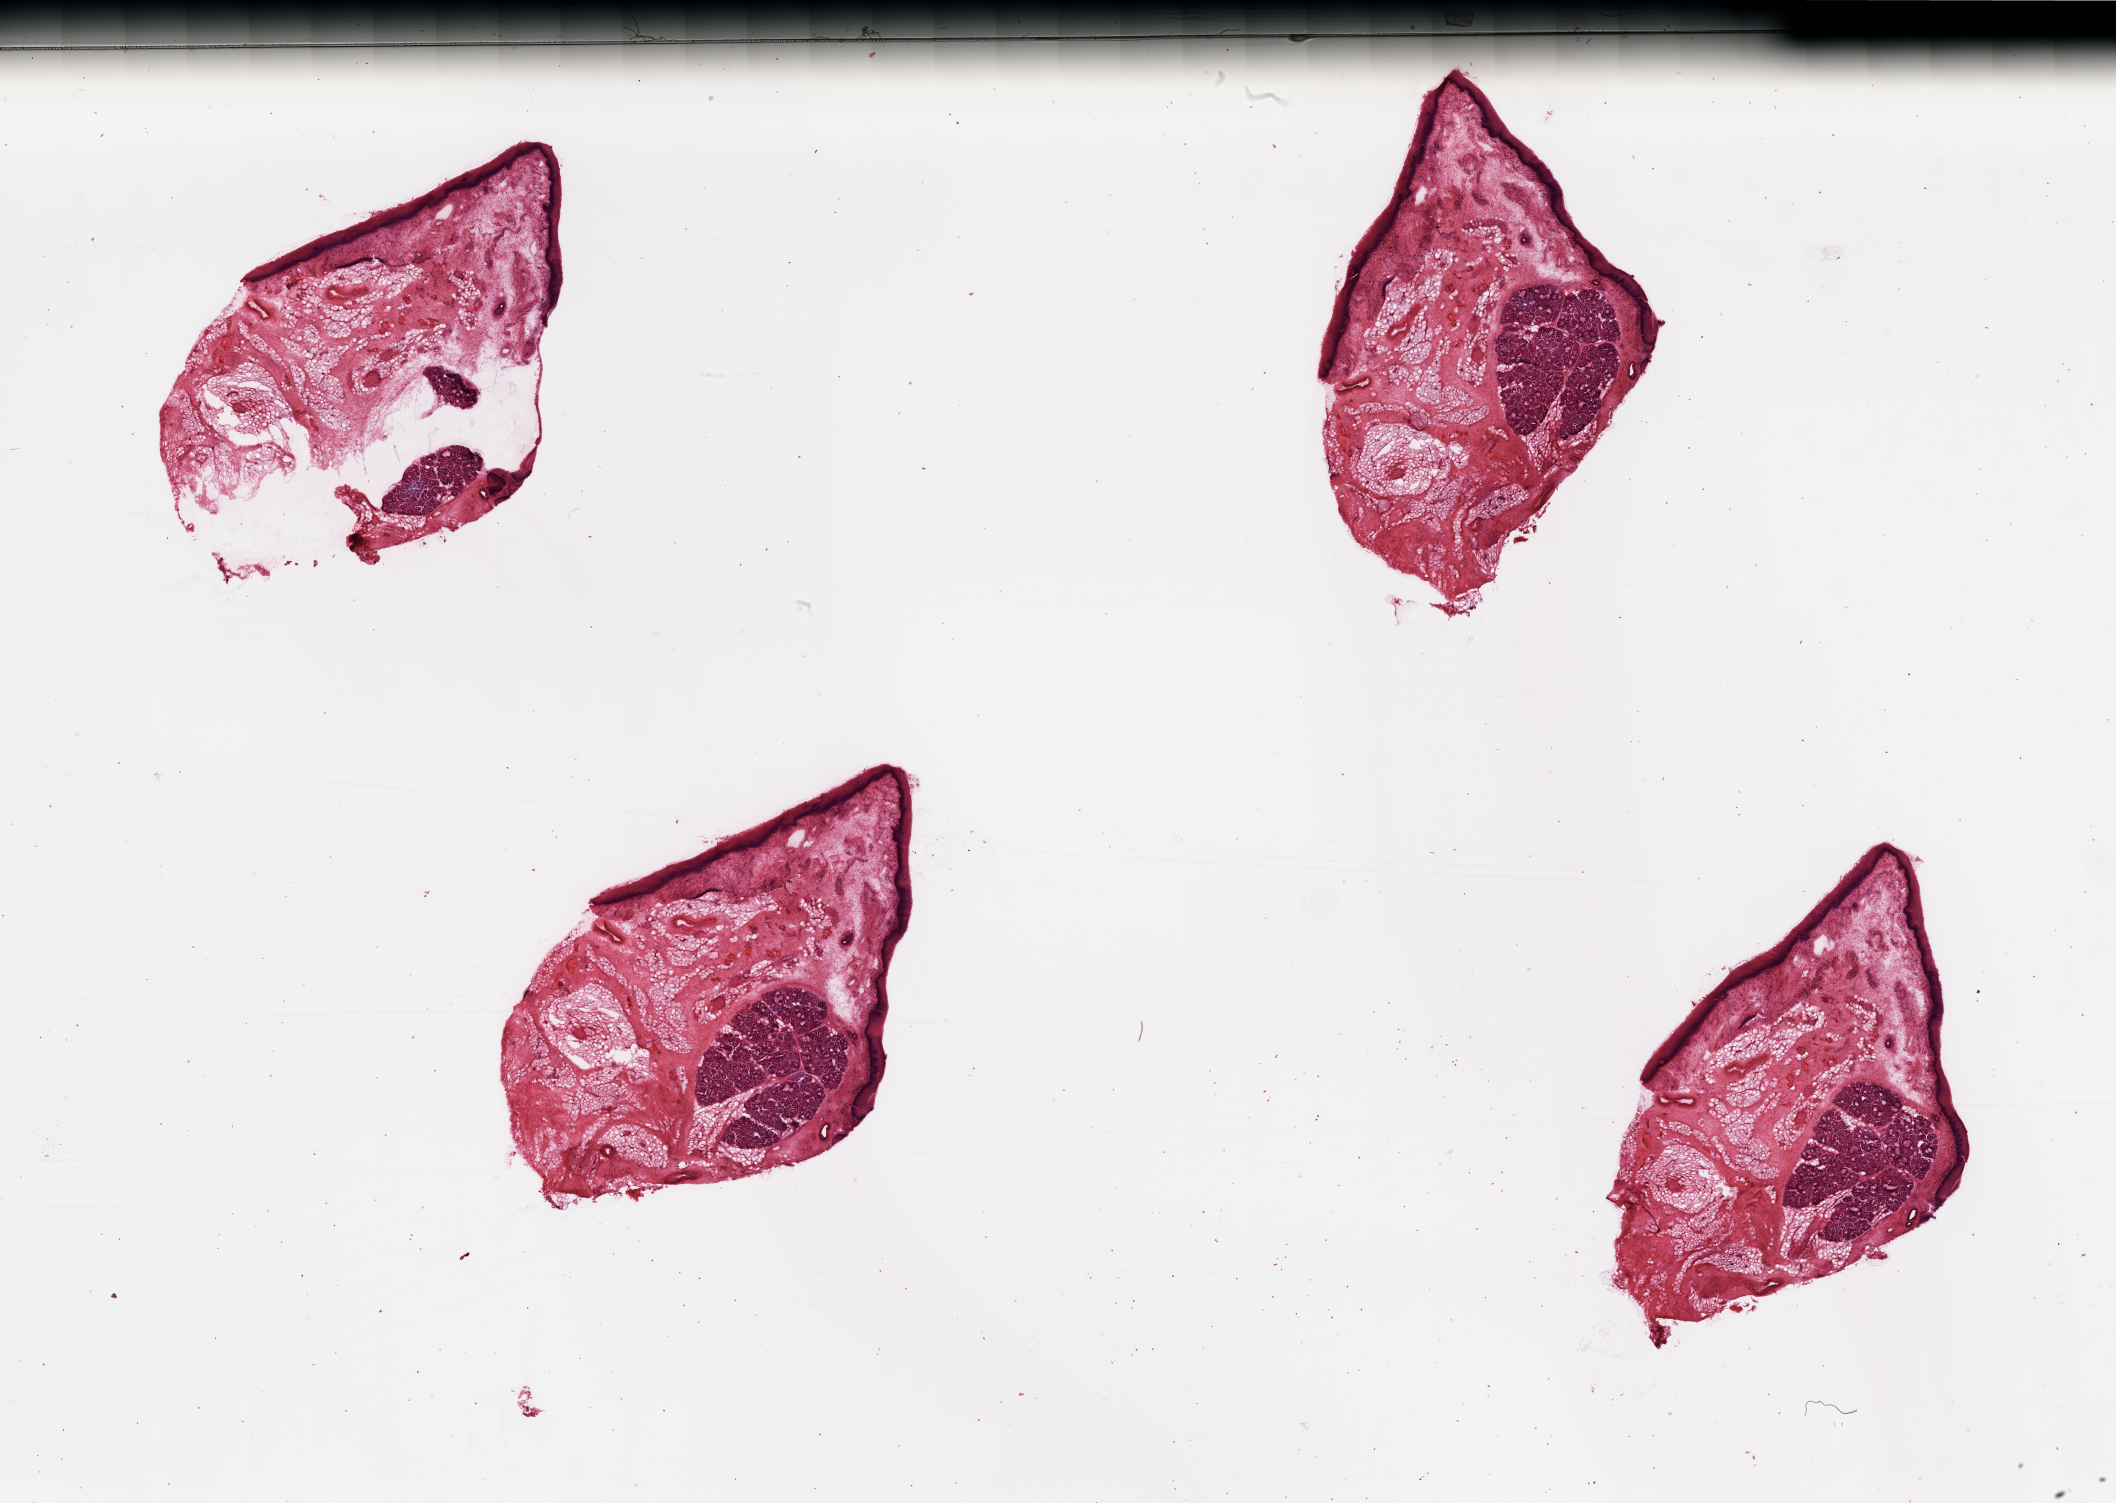
Digitized H&E-stained tissue section (whole slide), whole scanned area (about 33.5 x 23.8 mm) shown as a low-resolution overview, normal (non-tumour) tissue sample, sampled site: larynx. 67-year-old male patient.
* this section: normal (non-tumour) tissue from the same patient
* patient diagnosis: Squamous cell carcinoma, NOS